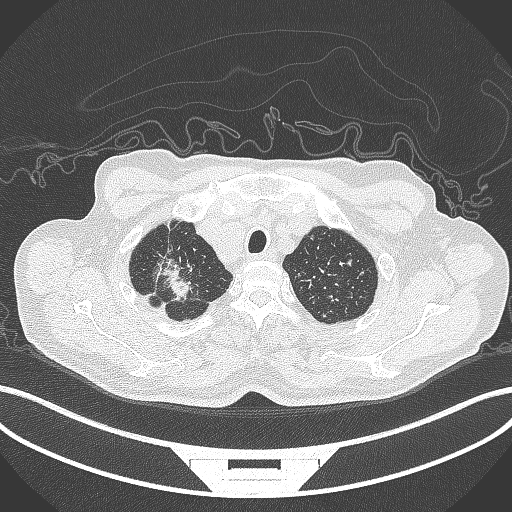
Chest CT, one axial slice. Slice 340 of 407 in the series (ordered by position). Reconstruction kernel B70f. Lung window (W 1500 / L -600 HU). 1 mm slice thickness. 512 × 512 image matrix, field of view 400 × 400 mm. Patient: male, 69 years. From the clinical record (not read from this slice): clinical TNM (as recorded): T1c N1 M1.
Structures marked on this image (rectangle marked by the reading radiologist):
- lung tumour (recorded histology: adenocarcinoma): bounding box (x1, y1, x2, y2) in pixels: (153, 253, 210, 308)